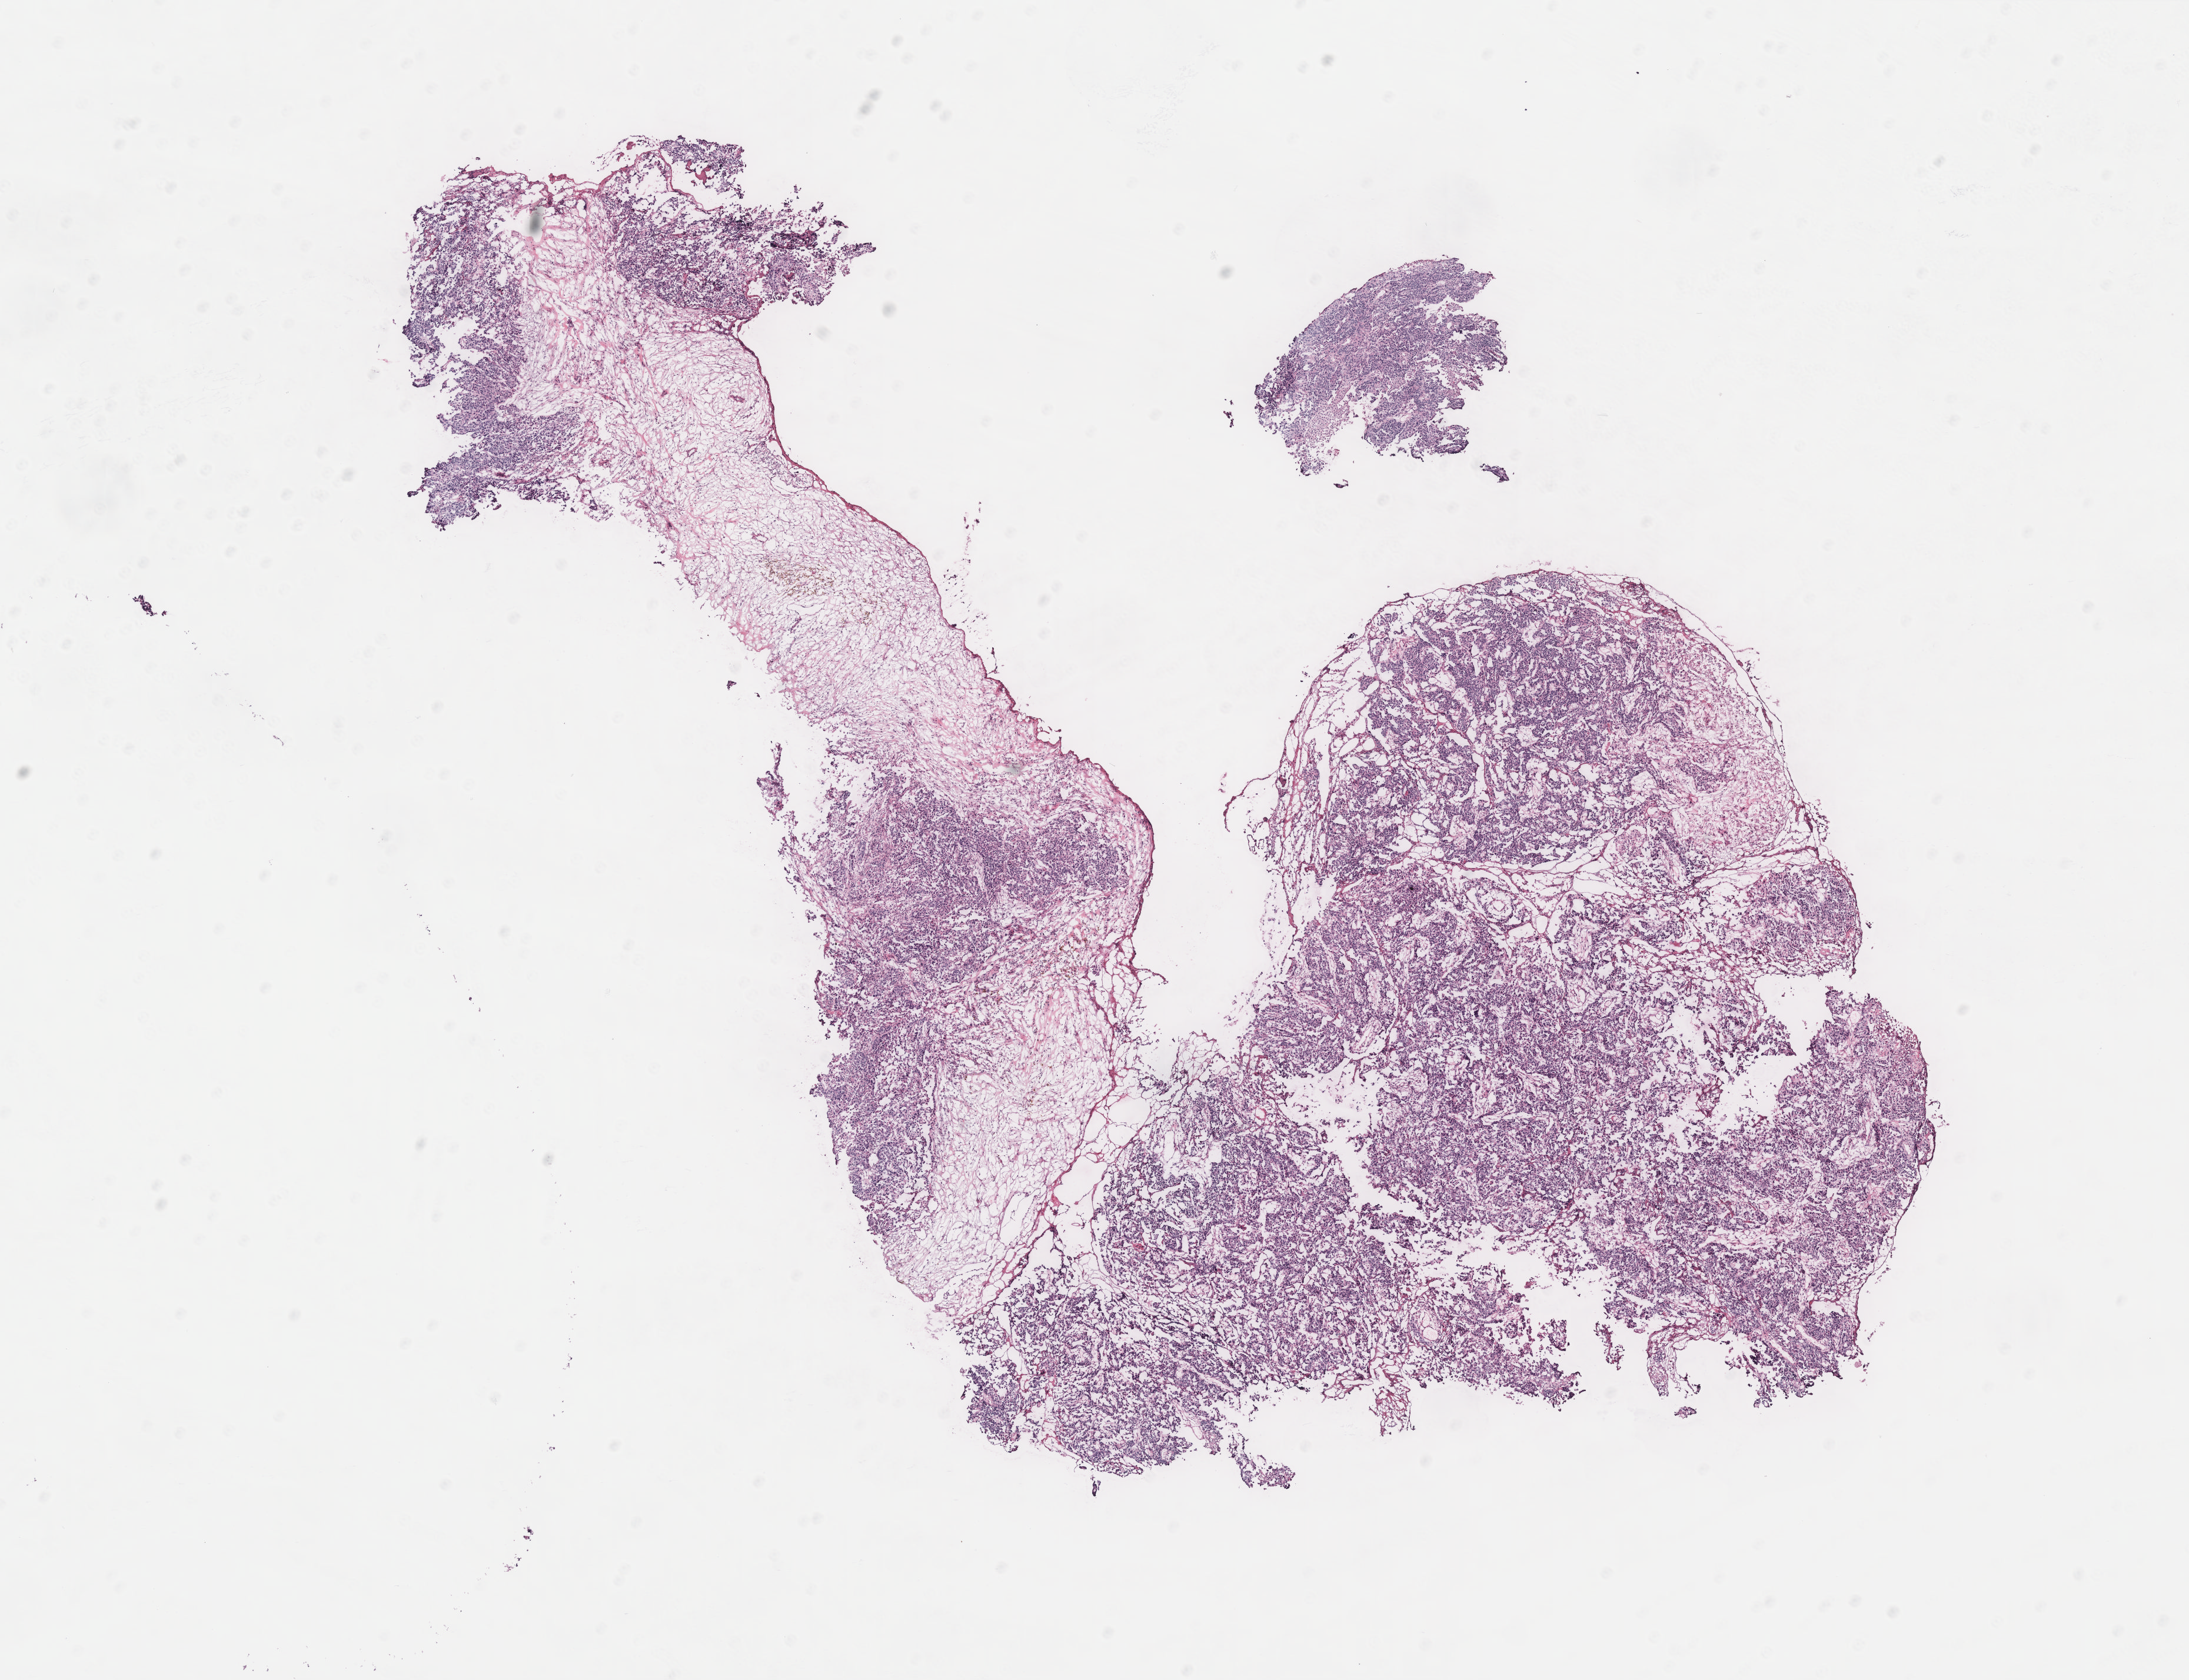
Hematoxylin and eosin (H&E) stained whole-slide image — low-resolution overview of the scanned area, about 14.9 x 11.4 mm (from a 40x scan), ovary, tumour tissue. Patient: female, age 66 years.
Histologic diagnosis: Serous adenocarcinoma, NOS (peritoneum, NOS). Primary tumour site (as recorded): peritoneum.